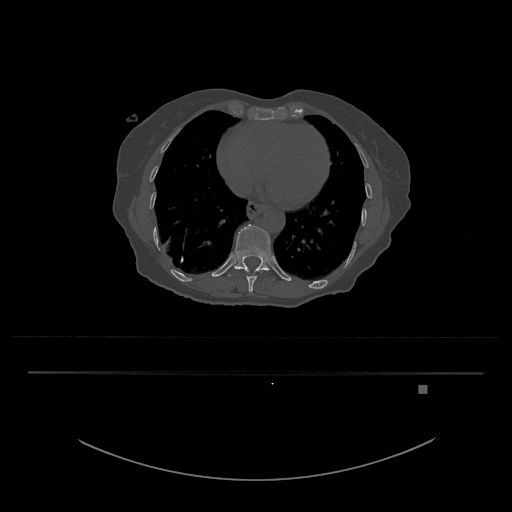
CT including the spine, one axial slice; slice 685 of 797 in the series (ordered by position); reconstruction kernel Br40s/3; 120 kVp; bone window (W 1800 / L 400 HU); 0.5 mm slice thickness; 512 × 512 image matrix. Patient: female, 57 years. Case-level facts recorded for this patient, not image findings: primary cancer: cervical.
Outlined on this slice (semi-automatic segmentation, software-assisted and operator-edited):
- T10 vertebra: bounding box [x1, y1, x2, y2] px = [243, 269, 263, 293]
- T11 vertebra: [228, 224, 271, 276]